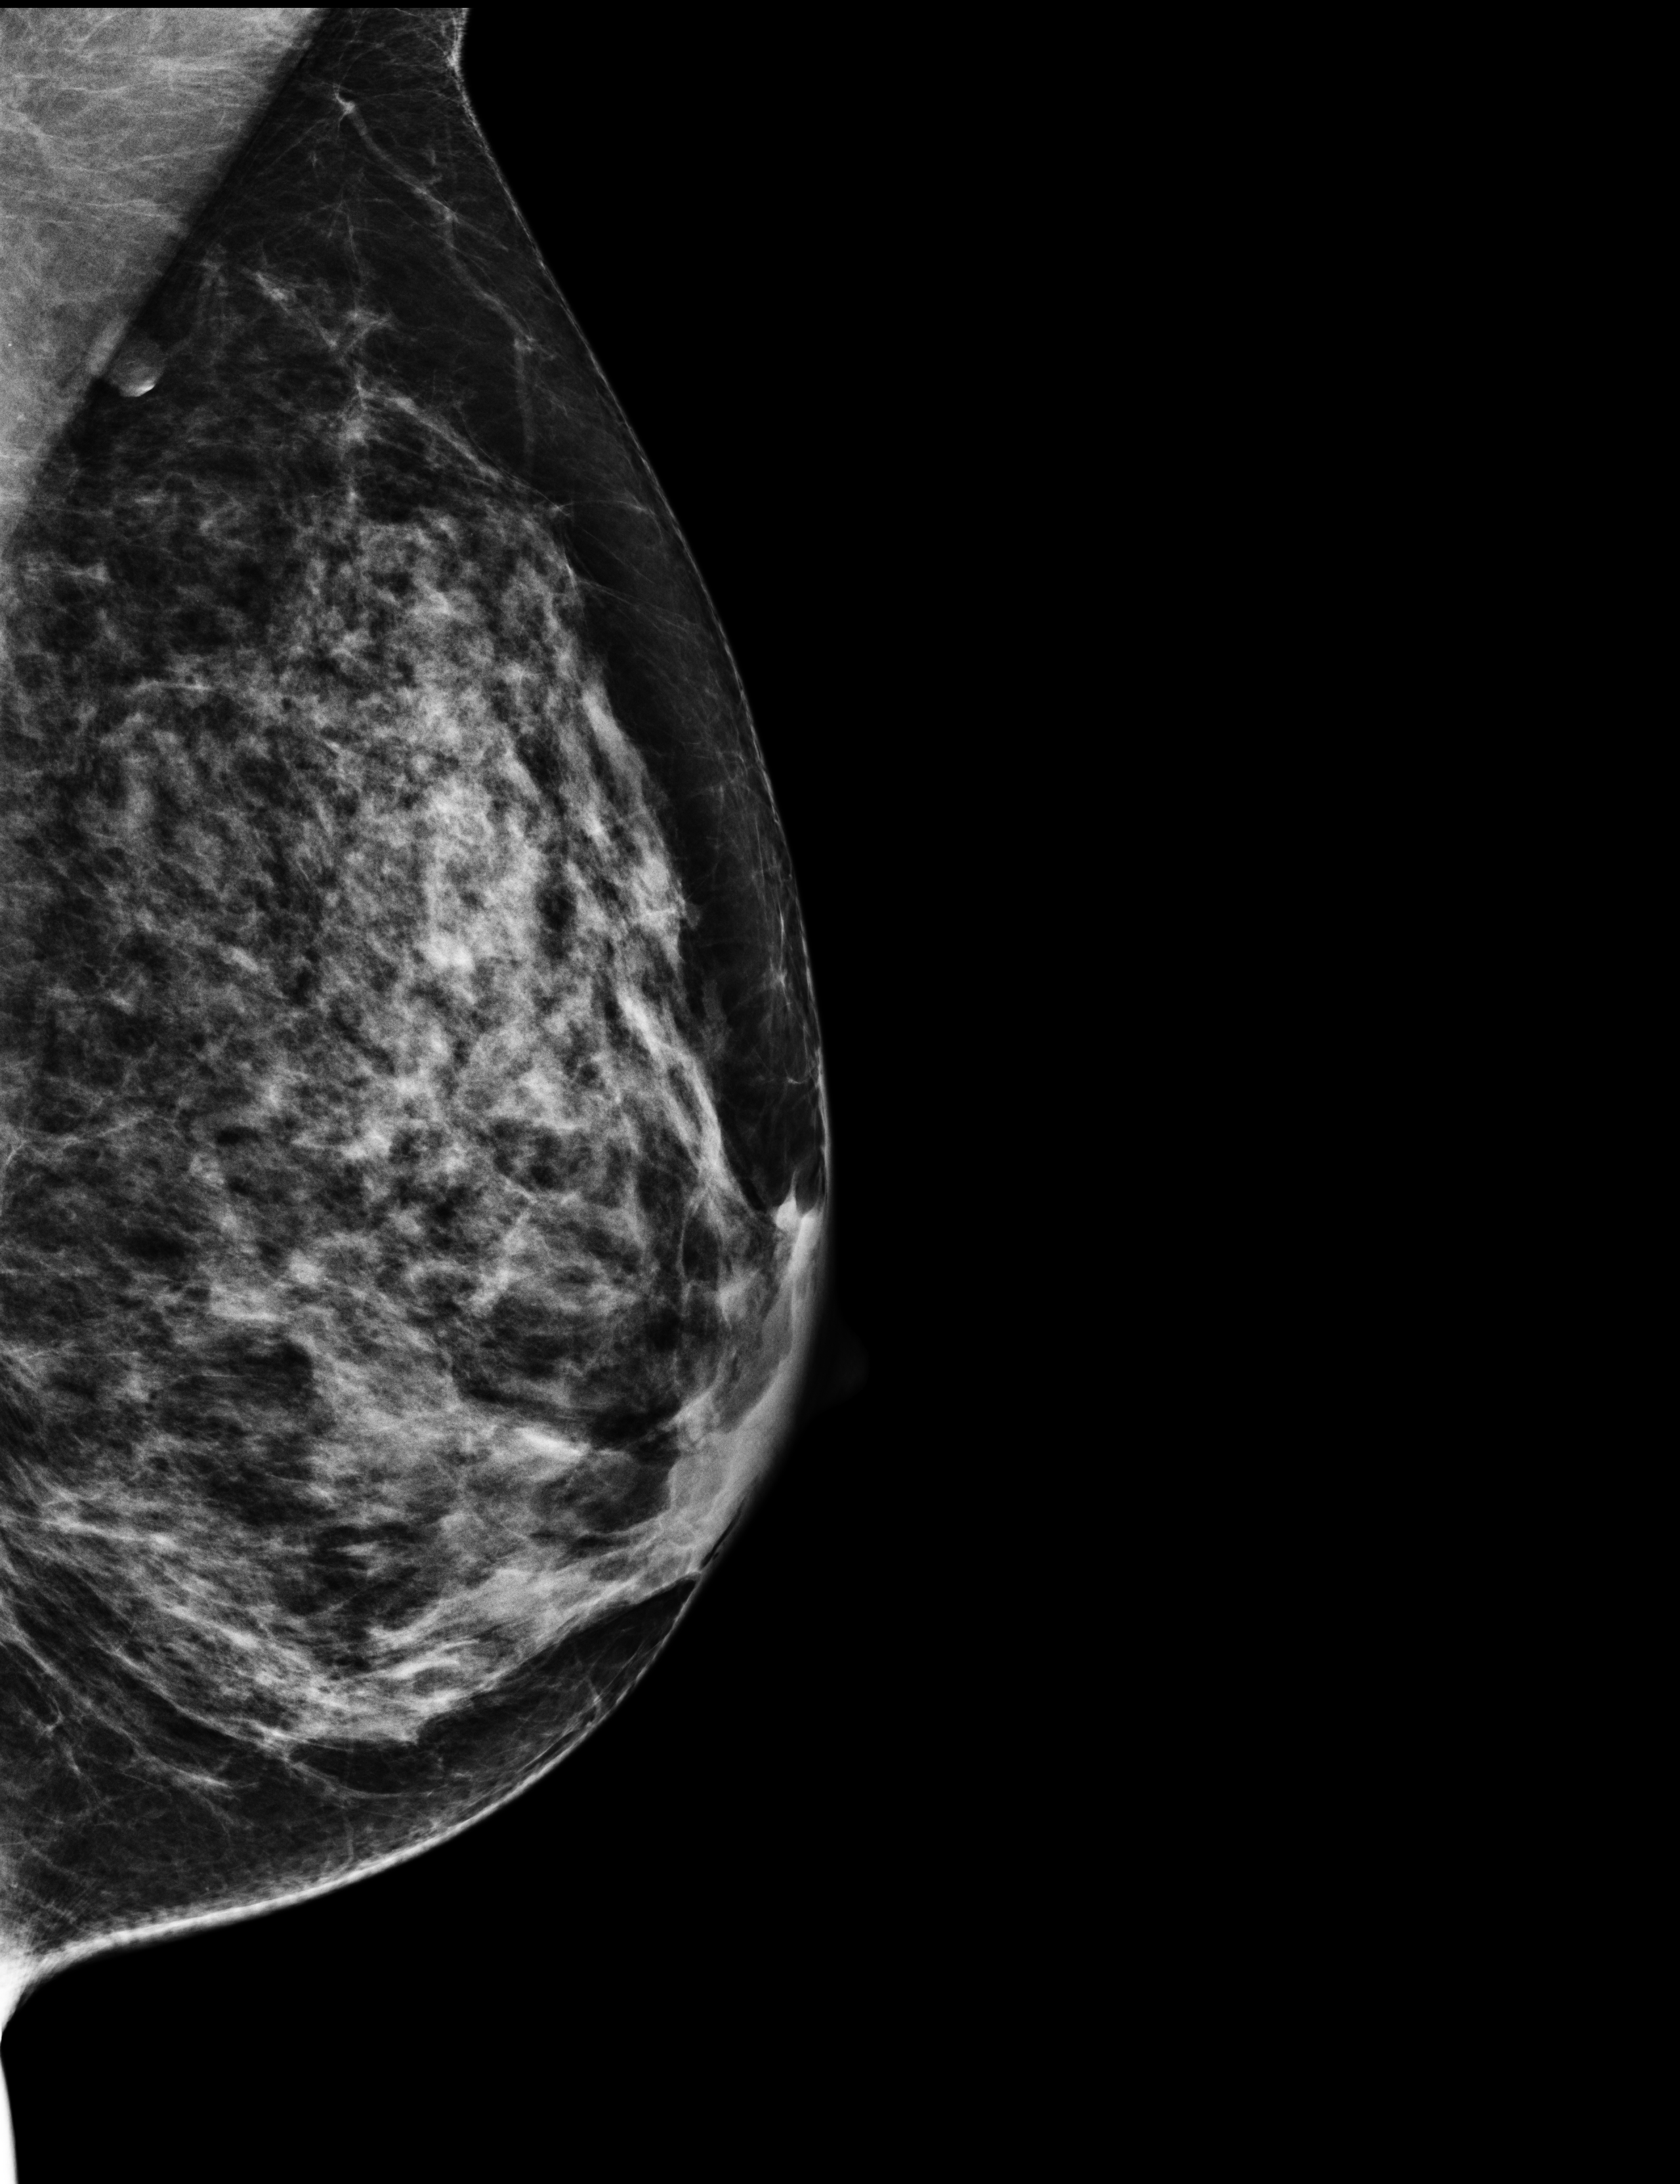
Screening examination; system: Selenia Dimensions.
Image type: full-field digital mammogram. Breast: left. Projection: MLO view.